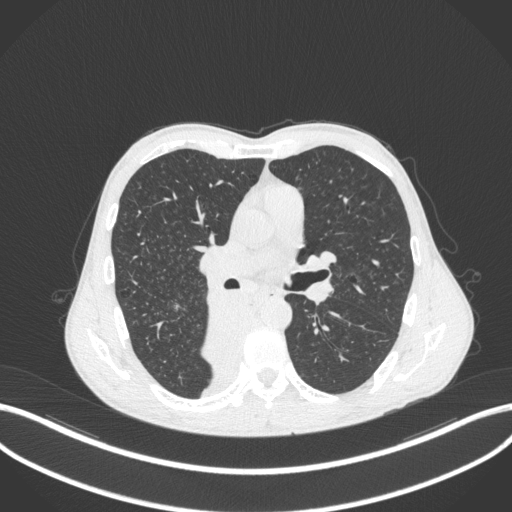
Chest CT, one axial slice. Position 216 of 371 along the scan axis. 120 kVp. Lung window (W 1500 / L -600 HU). 512 × 512 image matrix. Male patient, age 58 years. From the clinical record (not read from this slice): clinical TNM (as recorded): T3 N1 M1.
Structures marked on this image (rectangle marked by the reading radiologist):
- lung tumour (recorded histology: squamous cell carcinoma): bounding box (x1, y1, x2, y2) in pixels: (196, 294, 256, 387)